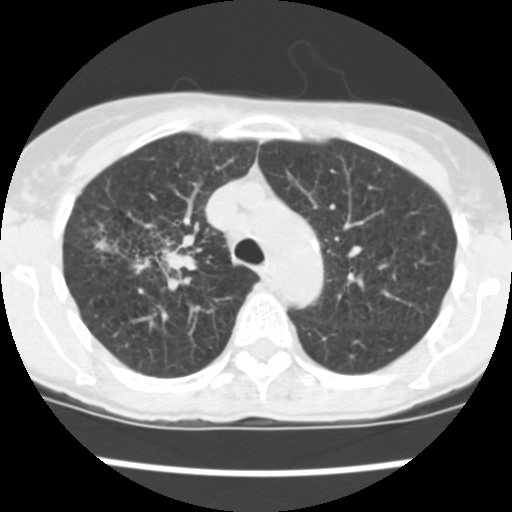
Low-dose screening chest CT, one axial slice. Slice 180 of 252 in the series (ordered by position). Reconstruction kernel STANDARD. Lung window (W 1500 / L -600 HU). 2.5 mm slice thickness. 512 × 512 image matrix, field of view 276 × 276 mm.
Outlined on this slice (expert manual segmentation):
- lesion 2 (tumor, lower lobe of right lung): box from (x=162, y=249) to (x=196, y=273) px